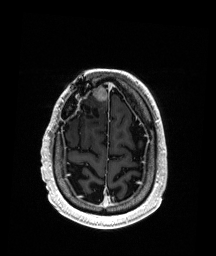
Brain MRI from a brain-tumour surgery series, one axial slice. Position 41 of 192 along the scan axis. T1-weighted post-contrast. 216 × 256 image matrix, field of view 211 × 250 mm. Case-level facts recorded for this patient, not image findings: histopathology: Astrocytoma; WHO grade: 3; IDH mutation: yes.
Outlined on this slice (outlined manually by an expert reader):
- previous resection cavity: bounding box <73,104,101,126> (left, top, right, bottom; pixels)
- tumour: <93,86,109,102>